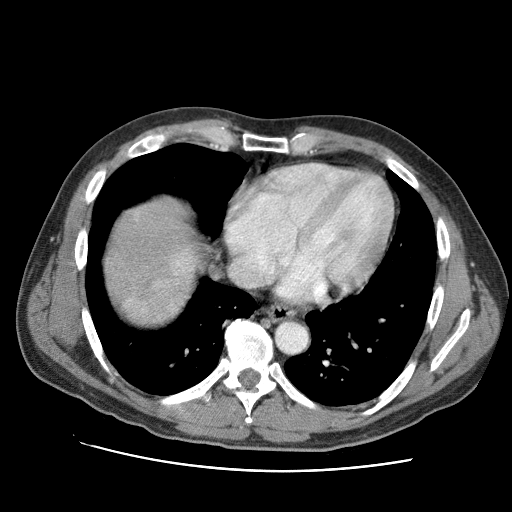
Contrast-enhanced abdominal CT (liver protocol), one axial slice; position 89 of 95 along the scan axis; one of 2 acquisitions stored at this slice position; soft-tissue window (W 400 / L 40 HU); 2.5 mm slice thickness; 512 × 512 image matrix, field of view 360 × 360 mm. Case-level facts recorded for this patient, not image findings: diagnosis: hepatocellular carcinoma (patient treated with transarterial chemoembolisation; whether this scan precedes or follows treatment is not stated here); TNM stage (as recorded): Stage-IVA; Child-Pugh class: A.
Outlined on this slice (semi-automatic segmentation, software-assisted and operator-edited):
- liver parenchyma outside the tumour (the mass and vessels are separate outlines, so this box may not span the whole liver): bounding box (x1, y1, x2, y2) in pixels: (104, 198, 196, 324)
- mass: (123, 248, 196, 322)